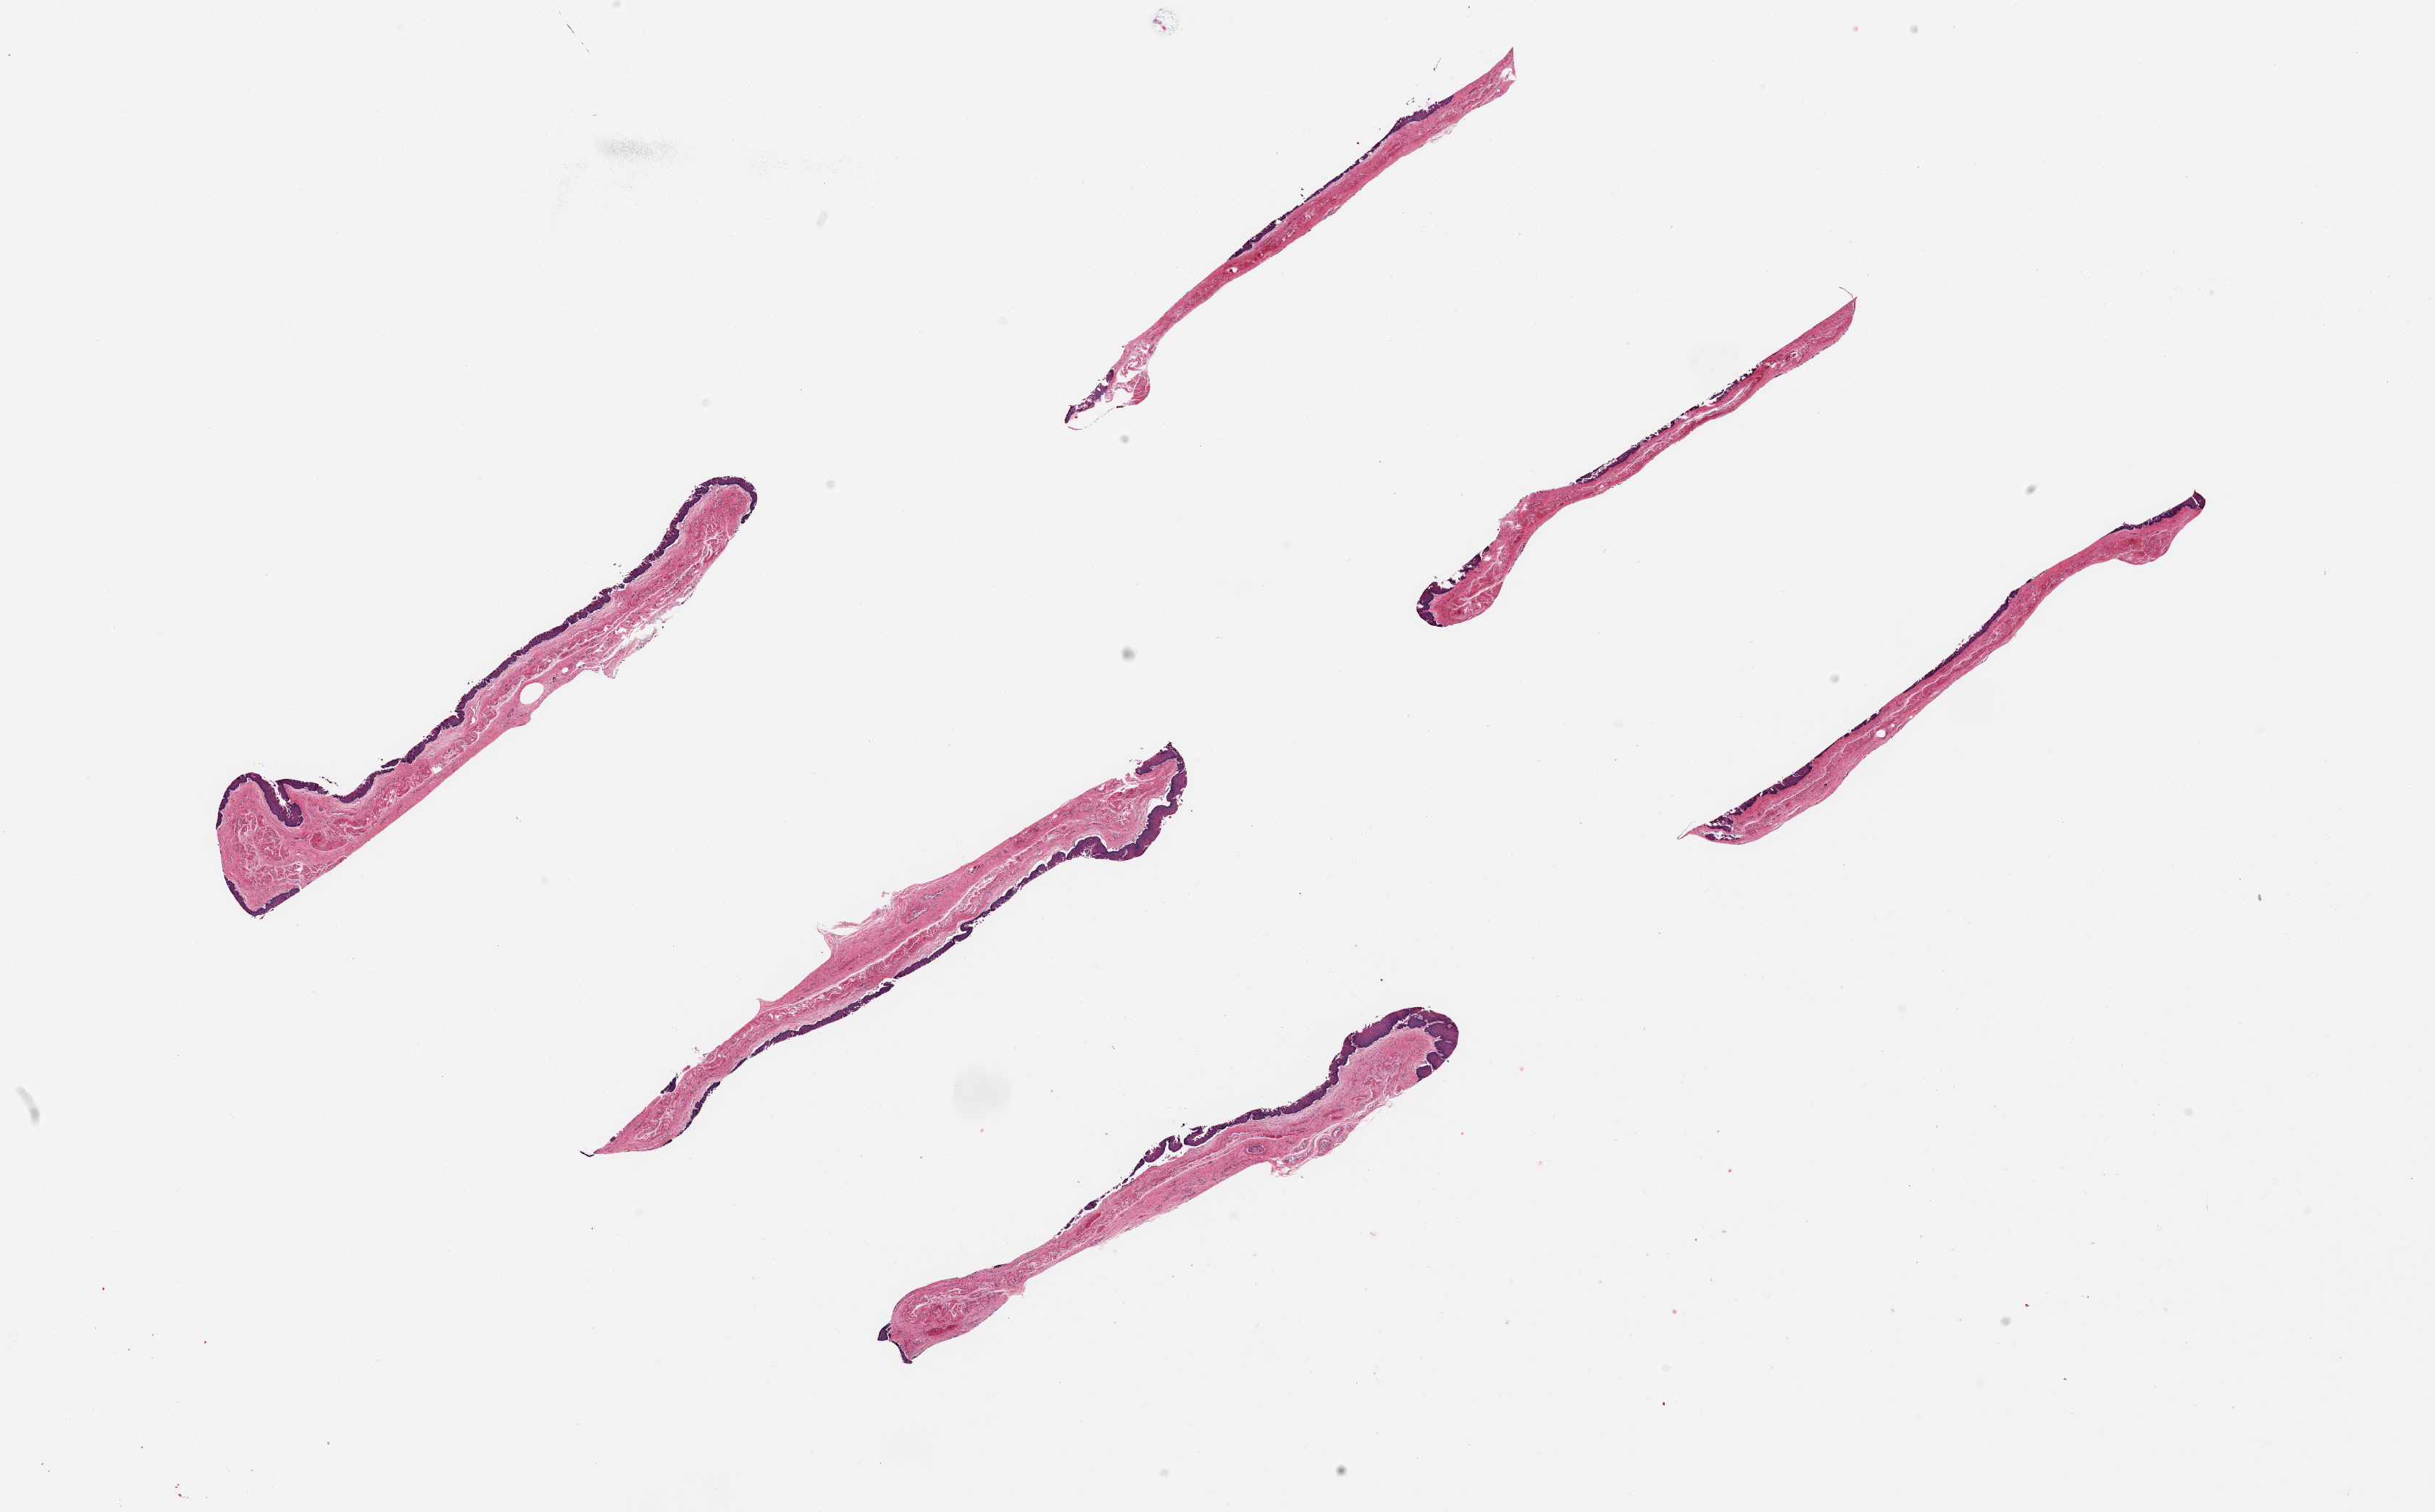
Whole-slide image, haematoxylin and eosin stain, brightfield, low-resolution overview of the scanned area, about 26.6 x 16.5 mm (acquisition: 20x scan). PAXgene-fixed paraffin-embedded (PFPE) section. Target tissue: esophageal mucous membrane. Donor tissue sample.
- reviewer comment on this tissue sample: 6 ~7x0.75mm pieces. Squamous mucosa is ~10% of thickness